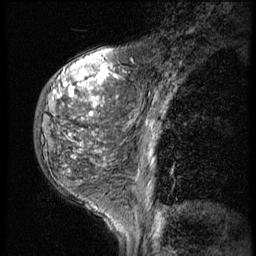
Breast MRI (dynamic contrast-enhanced), one sagittal slice; position 16 of 56 along the scan axis; 3 images stored at this slice position (order not interpretable as contrast timing); 1.5 T; TE 4.2 ms, TR 9 ms; 2.5 mm slice thickness; 256 × 256 image matrix, field of view 180 × 180 mm. Patient: female, 50 years. Case-level facts recorded for this patient, not image findings: setting: breast cancer imaged before/during neoadjuvant chemotherapy; receptor status: triple-negative.
Structures marked on this image (semi-automatic segmentation, software-assisted and operator-edited):
- analysis volume of interest (the breast-tissue region the enhancement analysis was run in; not a lesion): box from (x=33, y=50) to (x=116, y=191) px
- tumour enhancement mask (voxels above the 140 % enhancement threshold inside the analysis volume of interest): (x=54, y=70)–(x=116, y=116)